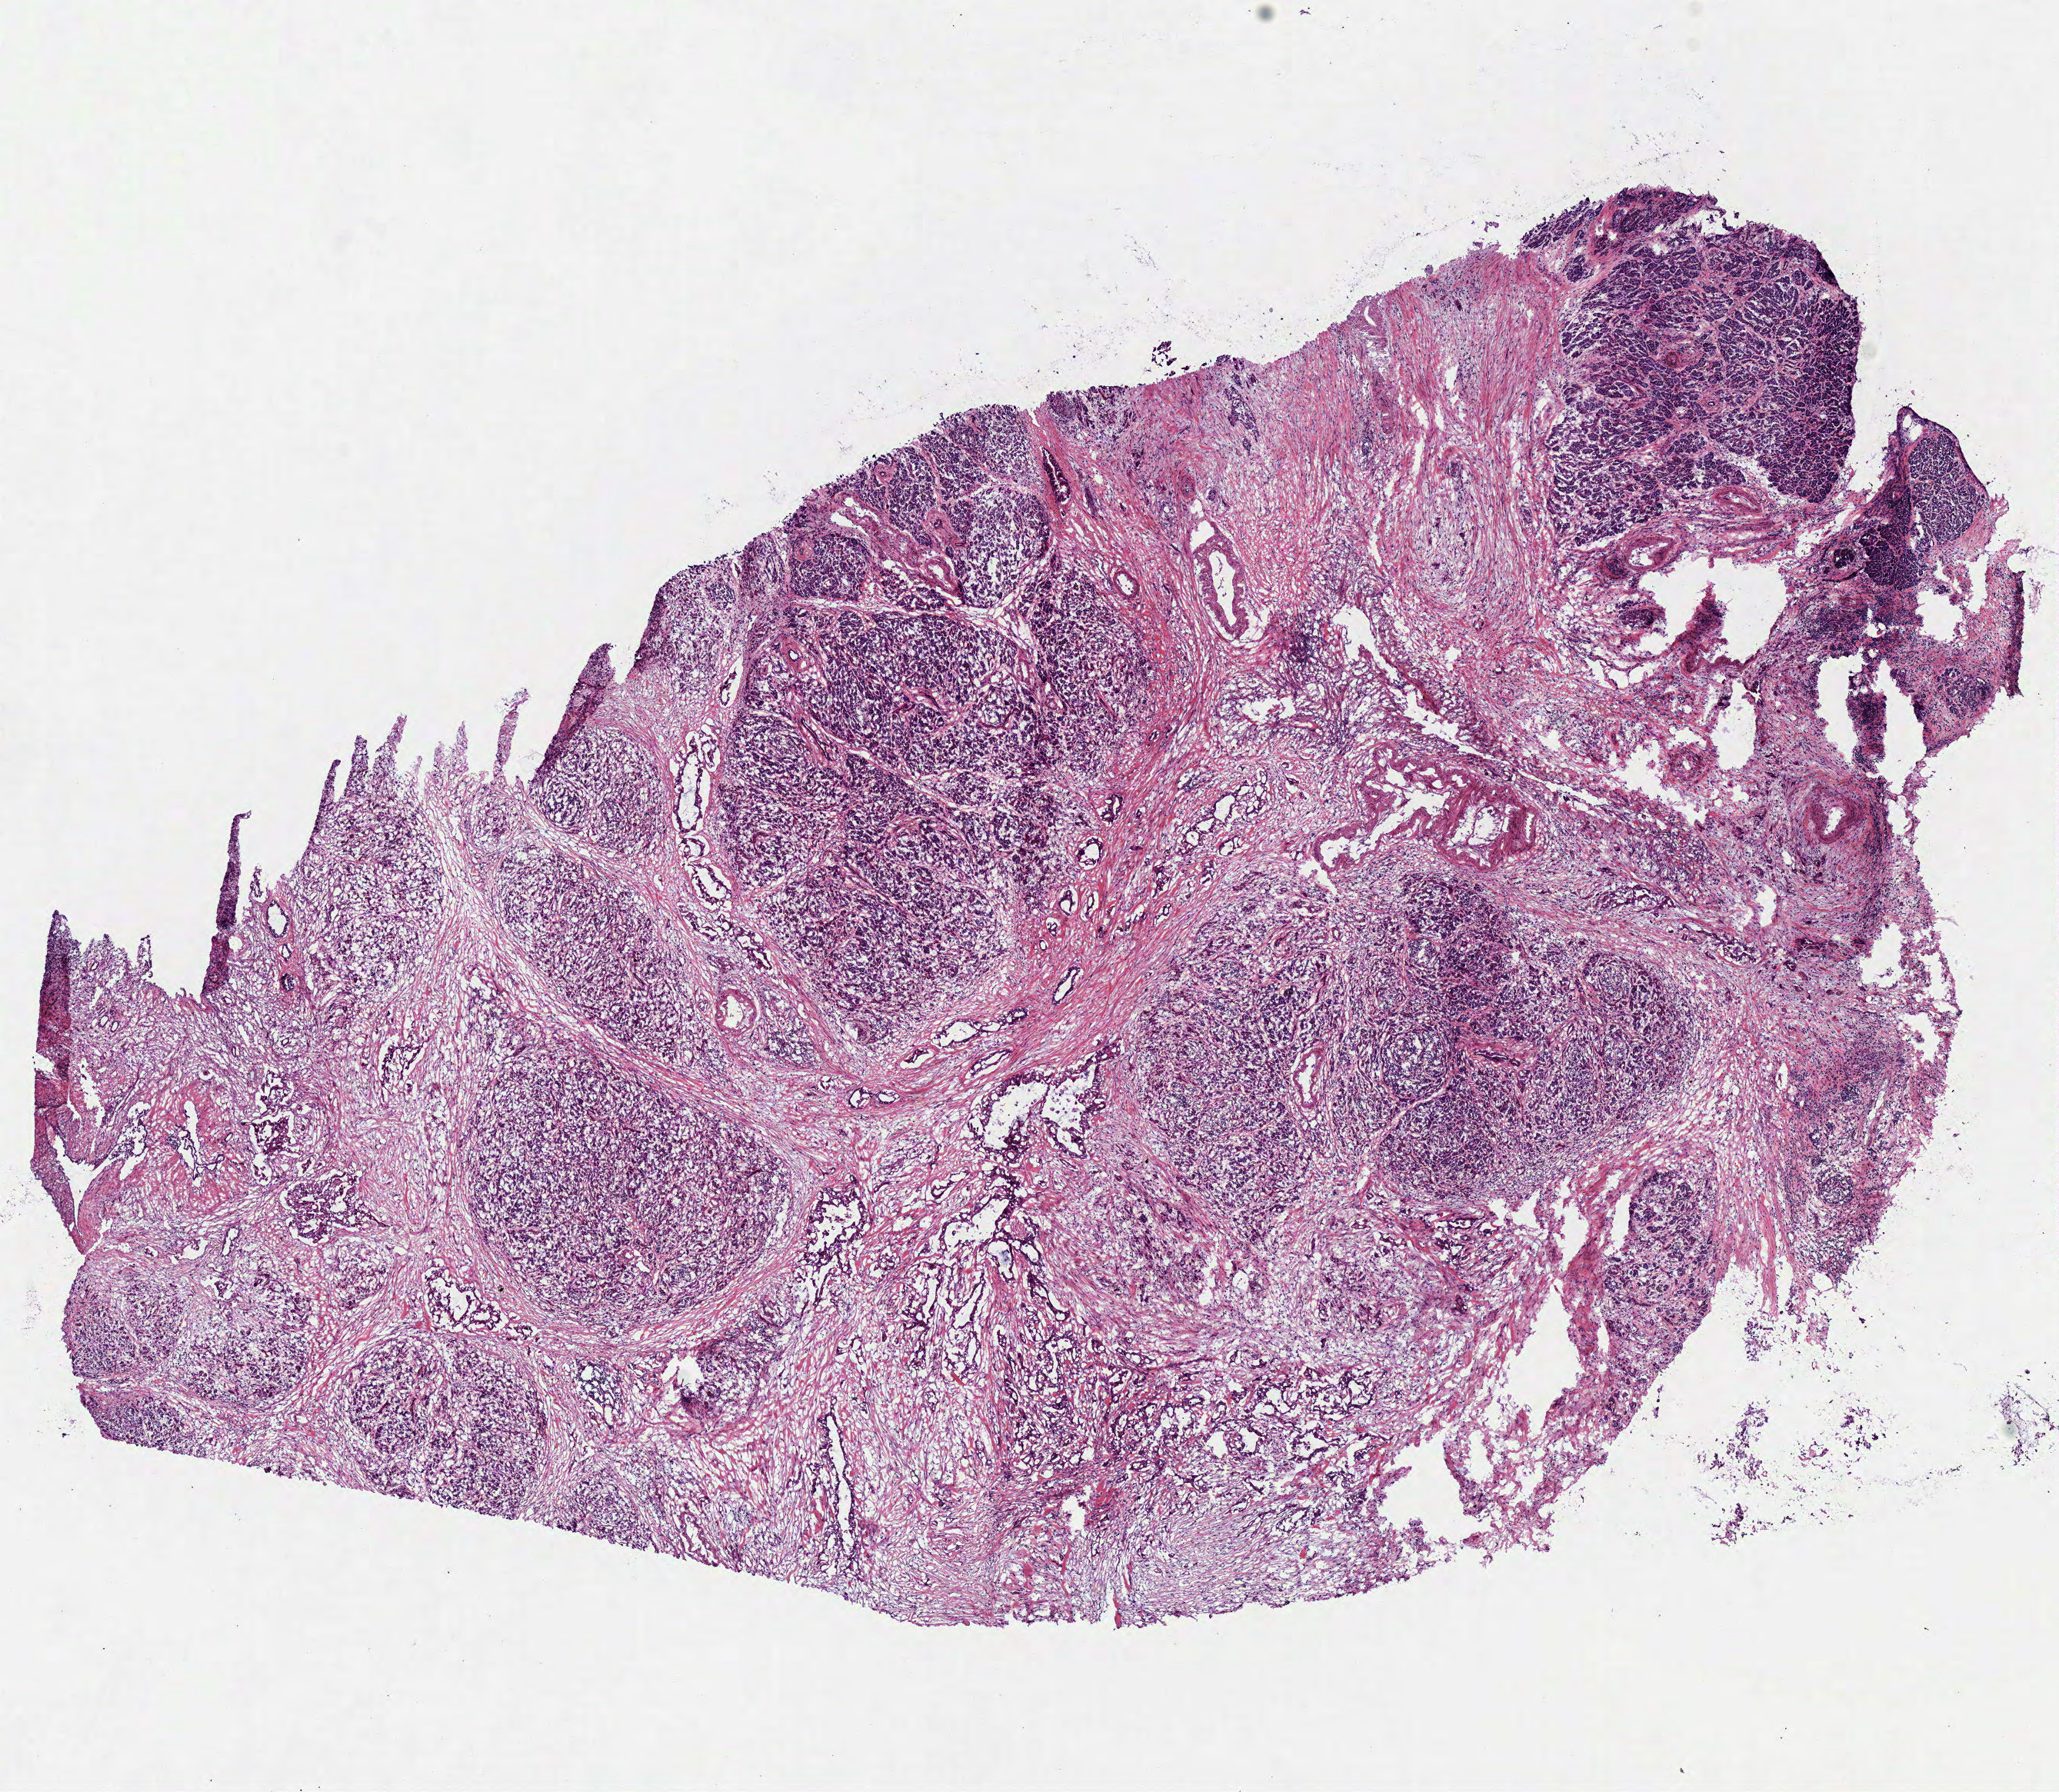
Hematoxylin and eosin (H&E) stained whole-slide image, shown as a low-resolution overview of the whole scanned area (about 10.5 x 9.2 mm), frozen section from the top of the tissue portion, sample: primary tumour, pancreas. Patient: female, age at initial diagnosis 73 years. Histologic grade: G2 (moderately differentiated). Pathologist review of this section (percent, as recorded): tumour cells 15%, tumour nuclei 10%, normal cells 70%, stromal cells 15%, necrosis 0%.
- AJCC pathologic stage: III (5th edition)
- histologic diagnosis: Infiltrating duct carcinoma, NOS